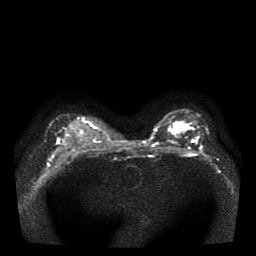
Breast MRI, one axial slice. Slice 26 of 41 in the series (ordered by position). Diffusion-weighted series; image 2 of 4 stored at this slice position (different b-values; order by instance number). 1.5 T. 5 mm slice thickness. 256 × 256 image matrix, field of view 330 × 330 mm. Female patient.
Structures marked on this image (expert manual segmentation):
- tumour on diffusion-weighted imaging: bounding box <174,127,187,133> (left, top, right, bottom; pixels)